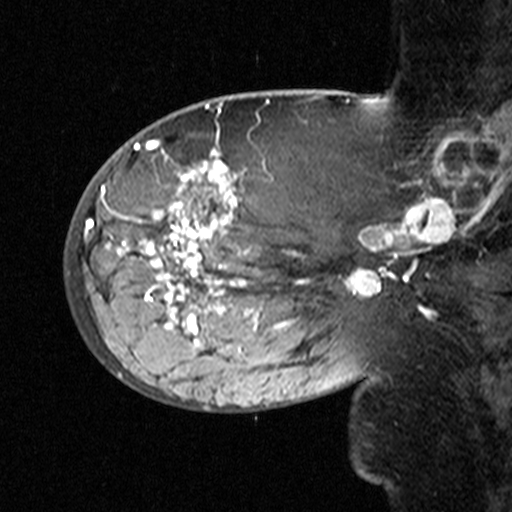
Breast MRI (dynamic contrast-enhanced), one sagittal slice; dynamic contrast-enhanced study with each time point stored as its own series, time point 2 of 3 at this slice position (early post-contrast, ordered by acquisition time); 1.5 T; TE 4.5 ms, TR 11 ms; 3 mm slice thickness; 512 × 512 image matrix, field of view 200 × 200 mm. Female patient, age 53 years. Case-level facts recorded for this patient, not image findings: setting: breast cancer imaged before/during neoadjuvant chemotherapy; receptor status: HR-positive, HER2-negative.
Outlined on this slice (semi-automatically segmented with operator editing):
- analysis volume of interest (the breast-tissue region the enhancement analysis was run in; not a lesion): bounding box <76,140,311,353> (left, top, right, bottom; pixels)
- tumour enhancement mask (voxels above the 90 % enhancement threshold inside the analysis volume of interest): <108,145,308,348>